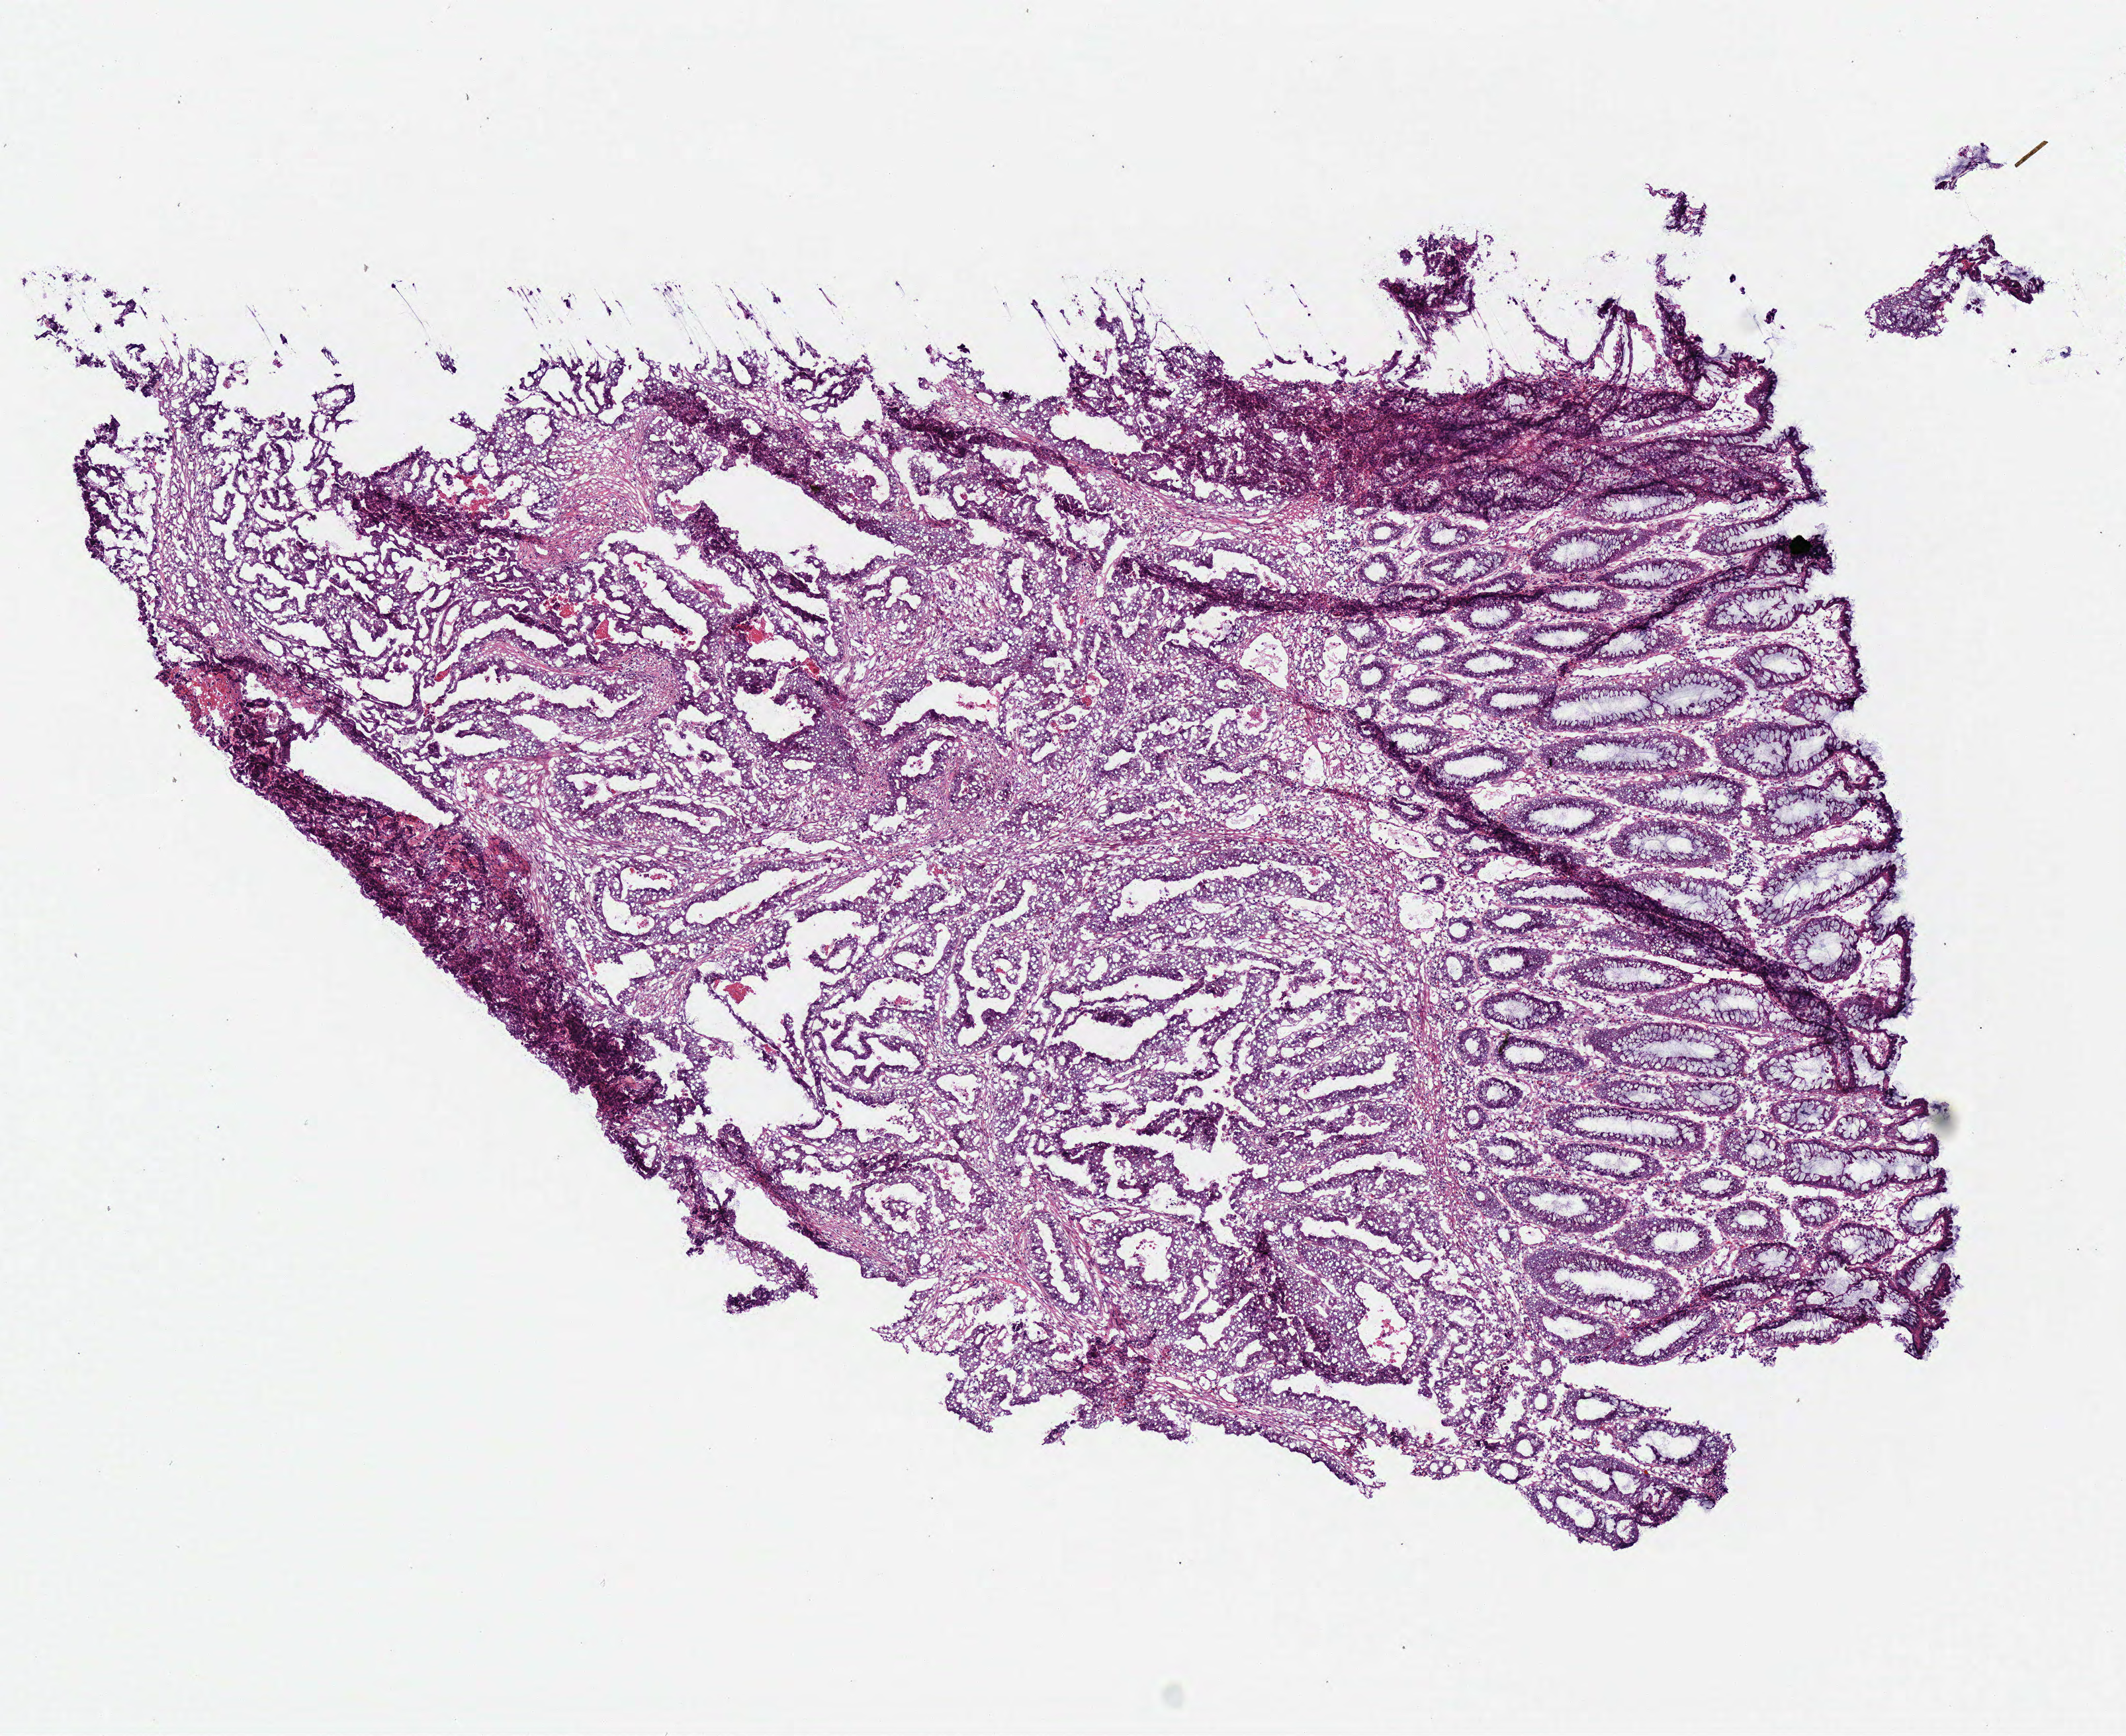
Hematoxylin and eosin (H&E) stained whole-slide image, shown as a low-resolution overview of the whole scanned area (about 6.3 x 5.2 mm, slide scanned at 40x). Frozen section from the bottom of the tissue portion. Primary tumour sample from the rectum. Male, age 72 years at initial diagnosis. Composition of this section per pathologist review: tumour cells 64%, tumour nuclei 71%, normal cells 33%, stromal cells 0%, necrosis 3%. Infiltration values recorded for this section: lymphocyte infiltration 15%, monocyte infiltration 2%, neutrophil infiltration 5%.
• TNM: T3 N1 MX
• histologic diagnosis: Adenocarcinoma, NOS (rectosigmoid junction)
• AJCC pathologic stage: IIIB
• lymph nodes positive (case pathology): 1 of 13 examined